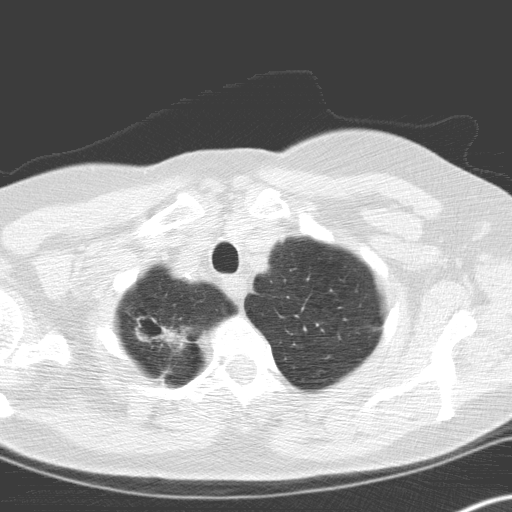
Low-dose screening chest CT, one axial slice; lung window (W 1500 / L -600 HU); 512 × 512 image matrix, field of view 306 × 306 mm.
Structures marked on this image (expert manual segmentation):
- lesion 1 (tumor, upper lobe of right lung): bounding box (x1, y1, x2, y2) in pixels: (159, 325, 184, 349)